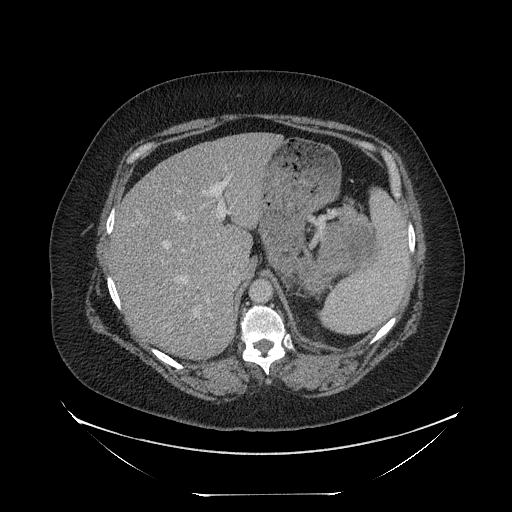
Contrast-enhanced abdominal CT, one axial slice; slice 165 of 205 in the series (ordered by position); 120 kVp; soft-tissue window (W 400 / L 40 HU); 2.5 mm slice thickness; 512 × 512 image matrix. Female patient, age 53 years. From the clinical record (not read from this slice): diagnosis: adrenocortical carcinoma; tumour side: left adrenal; tumour size at pathology: 17 cm.
Outlined on this slice (semi-automatically segmented with operator editing):
- mass: bounding box <298,225,373,291> (left, top, right, bottom; pixels)